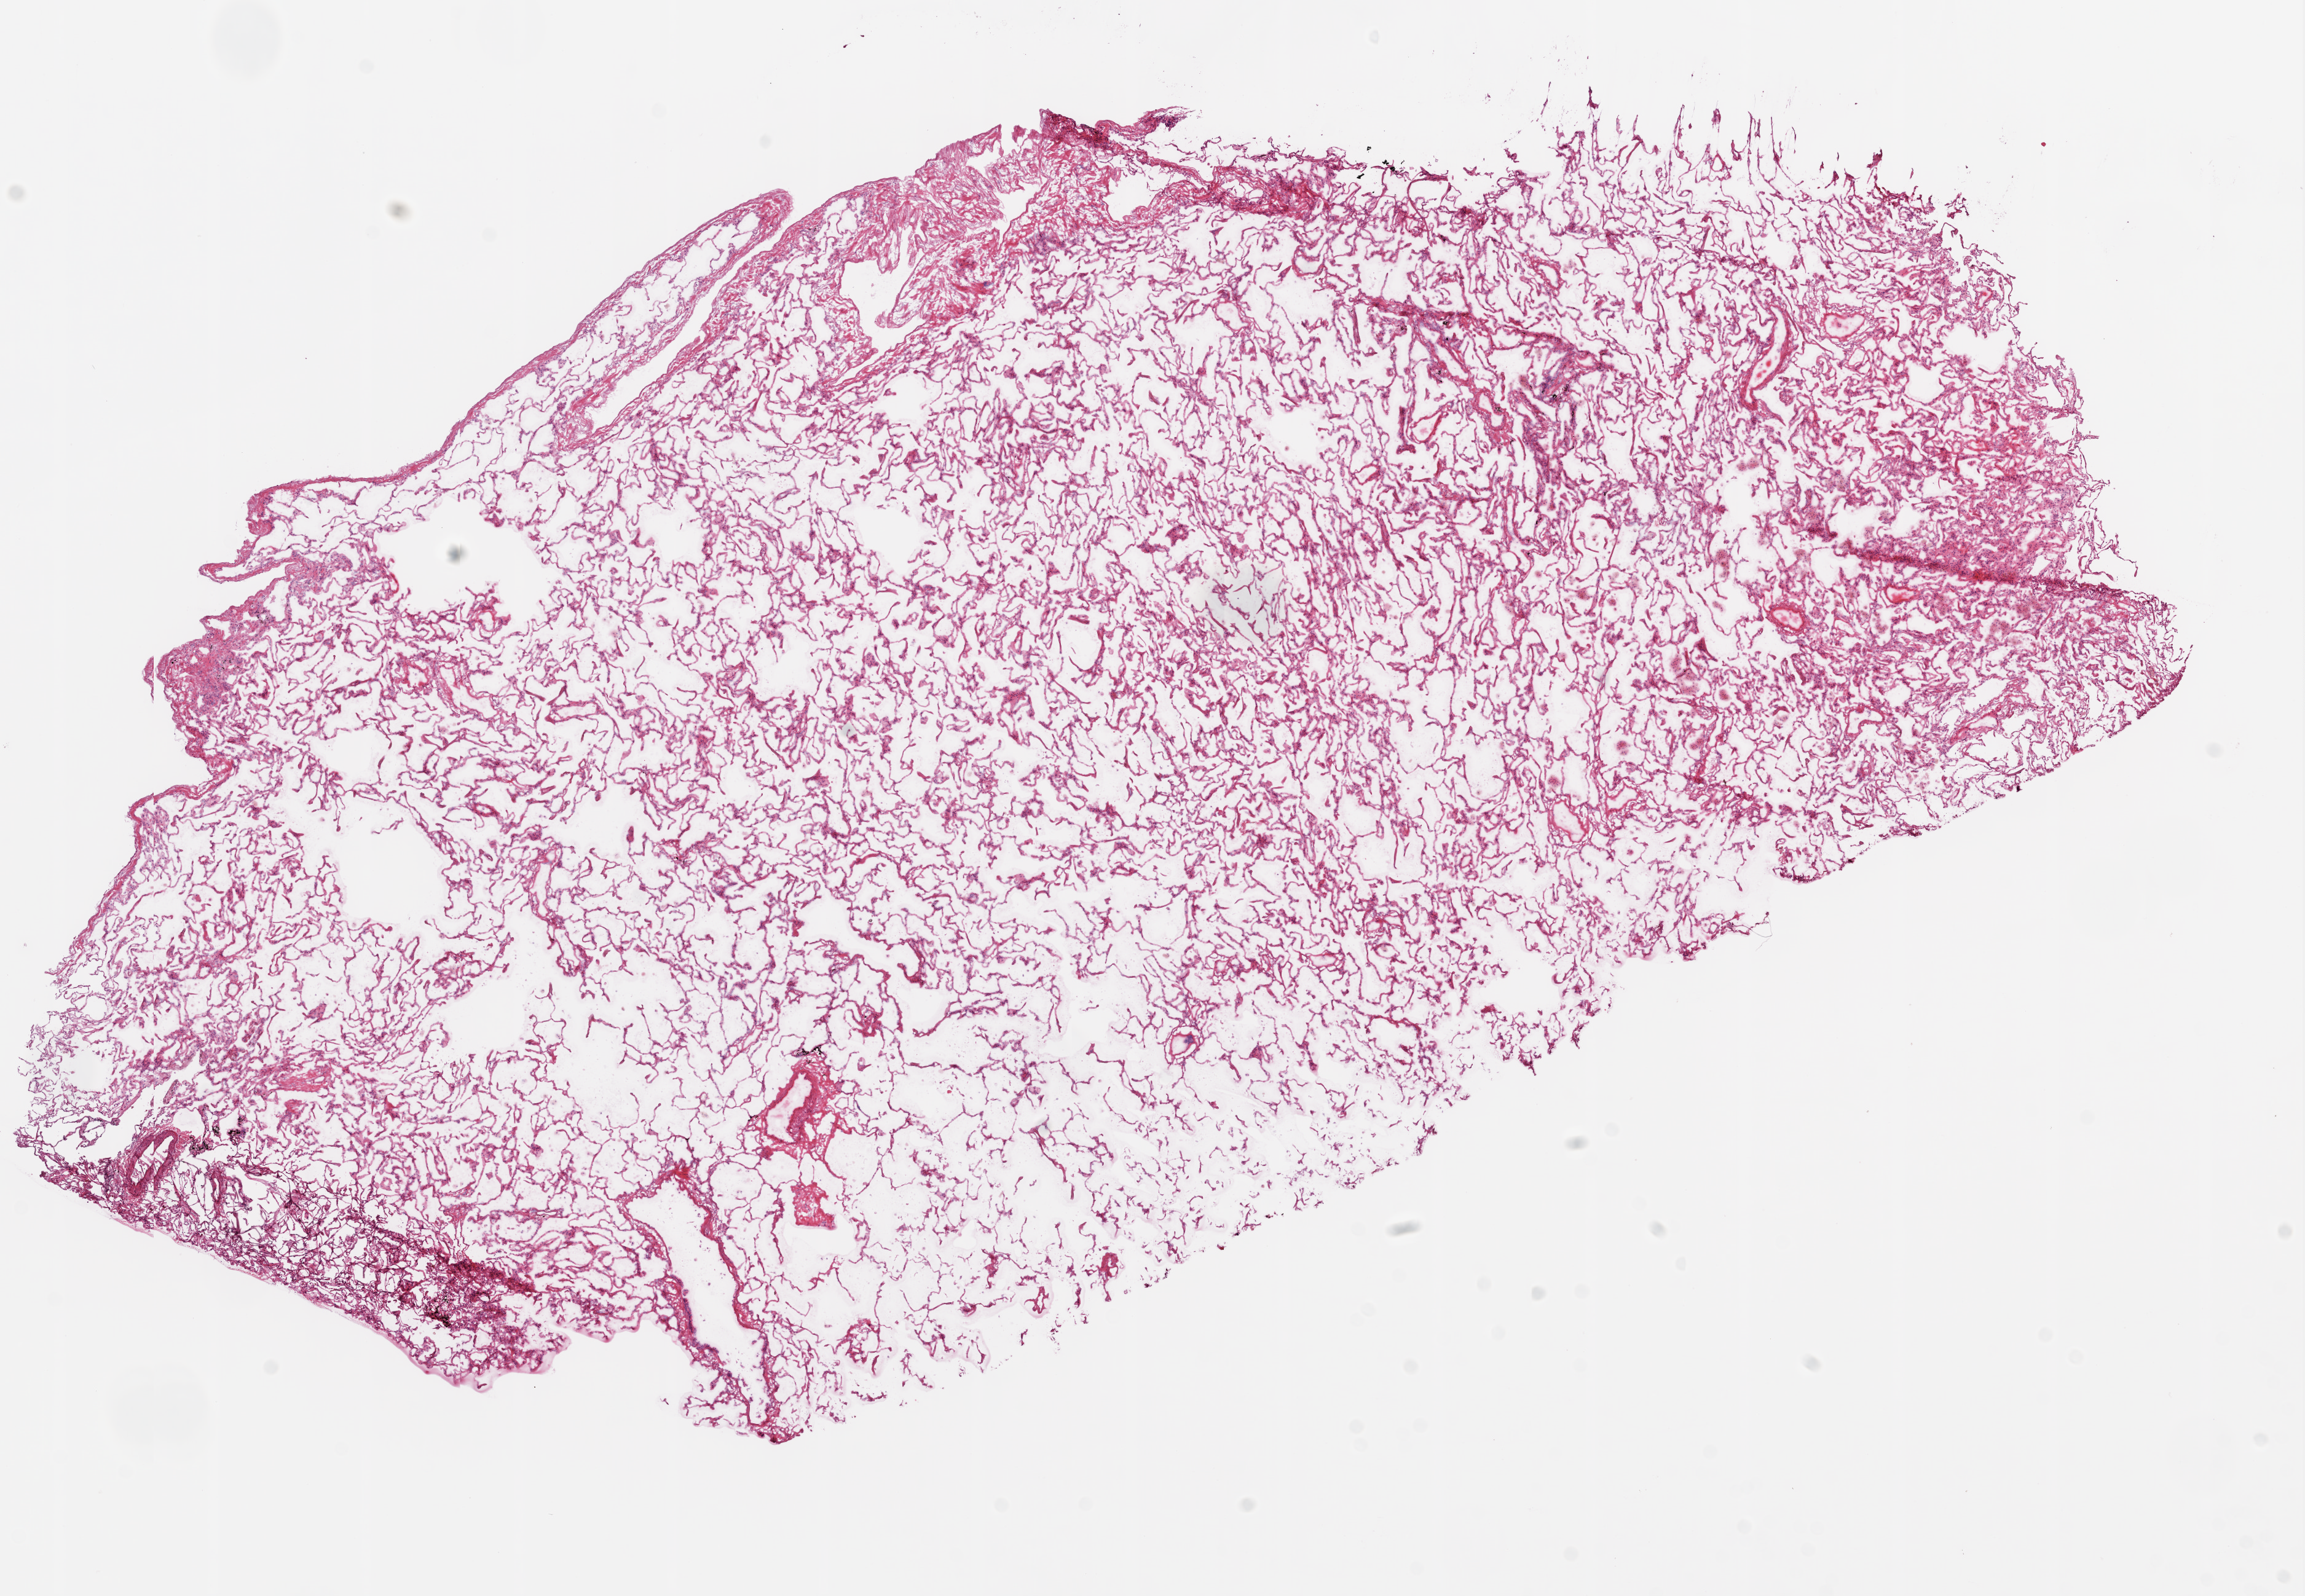
Whole-slide histology image, Hematoxylin and eosin (H&E) stained — a low-resolution overview of the entire scanned area, about 15.0 x 10.4 mm (acquisition: 20x scan), frozen section from the top of the tissue portion, sample: solid tissue normal (non-tumour tissue), lung. Male patient; age at initial diagnosis 74 years.
This section: solid tissue normal sample (biorepository sample class). Patient diagnosis: Squamous cell carcinoma, NOS (lower lobe, lung).